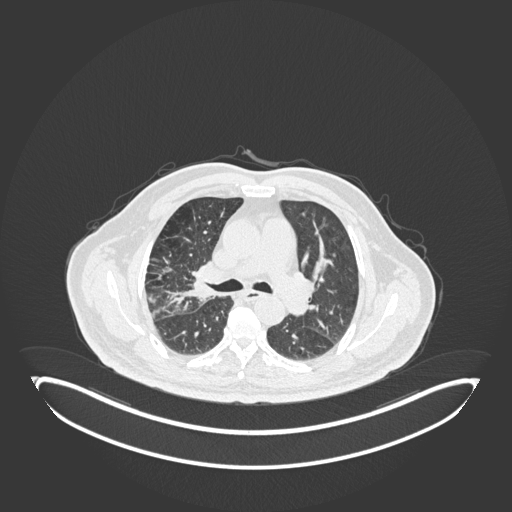
Chest CT, one axial slice; position 108 of 247 along the scan axis; reconstruction kernel B30f; 120 kVp; lung window (W 1500 / L -600 HU); 1 mm slice thickness; 512 × 512 image matrix, field of view 500 × 500 mm. Male patient, age 72 years. From the clinical record (not read from this slice): clinical TNM (as recorded): T1c N0 M0.
Structures marked on this image (rectangle marked by the reading radiologist):
- lung tumour (recorded histology: squamous cell carcinoma): bounding box (x1, y1, x2, y2) in pixels: (179, 260, 213, 305)